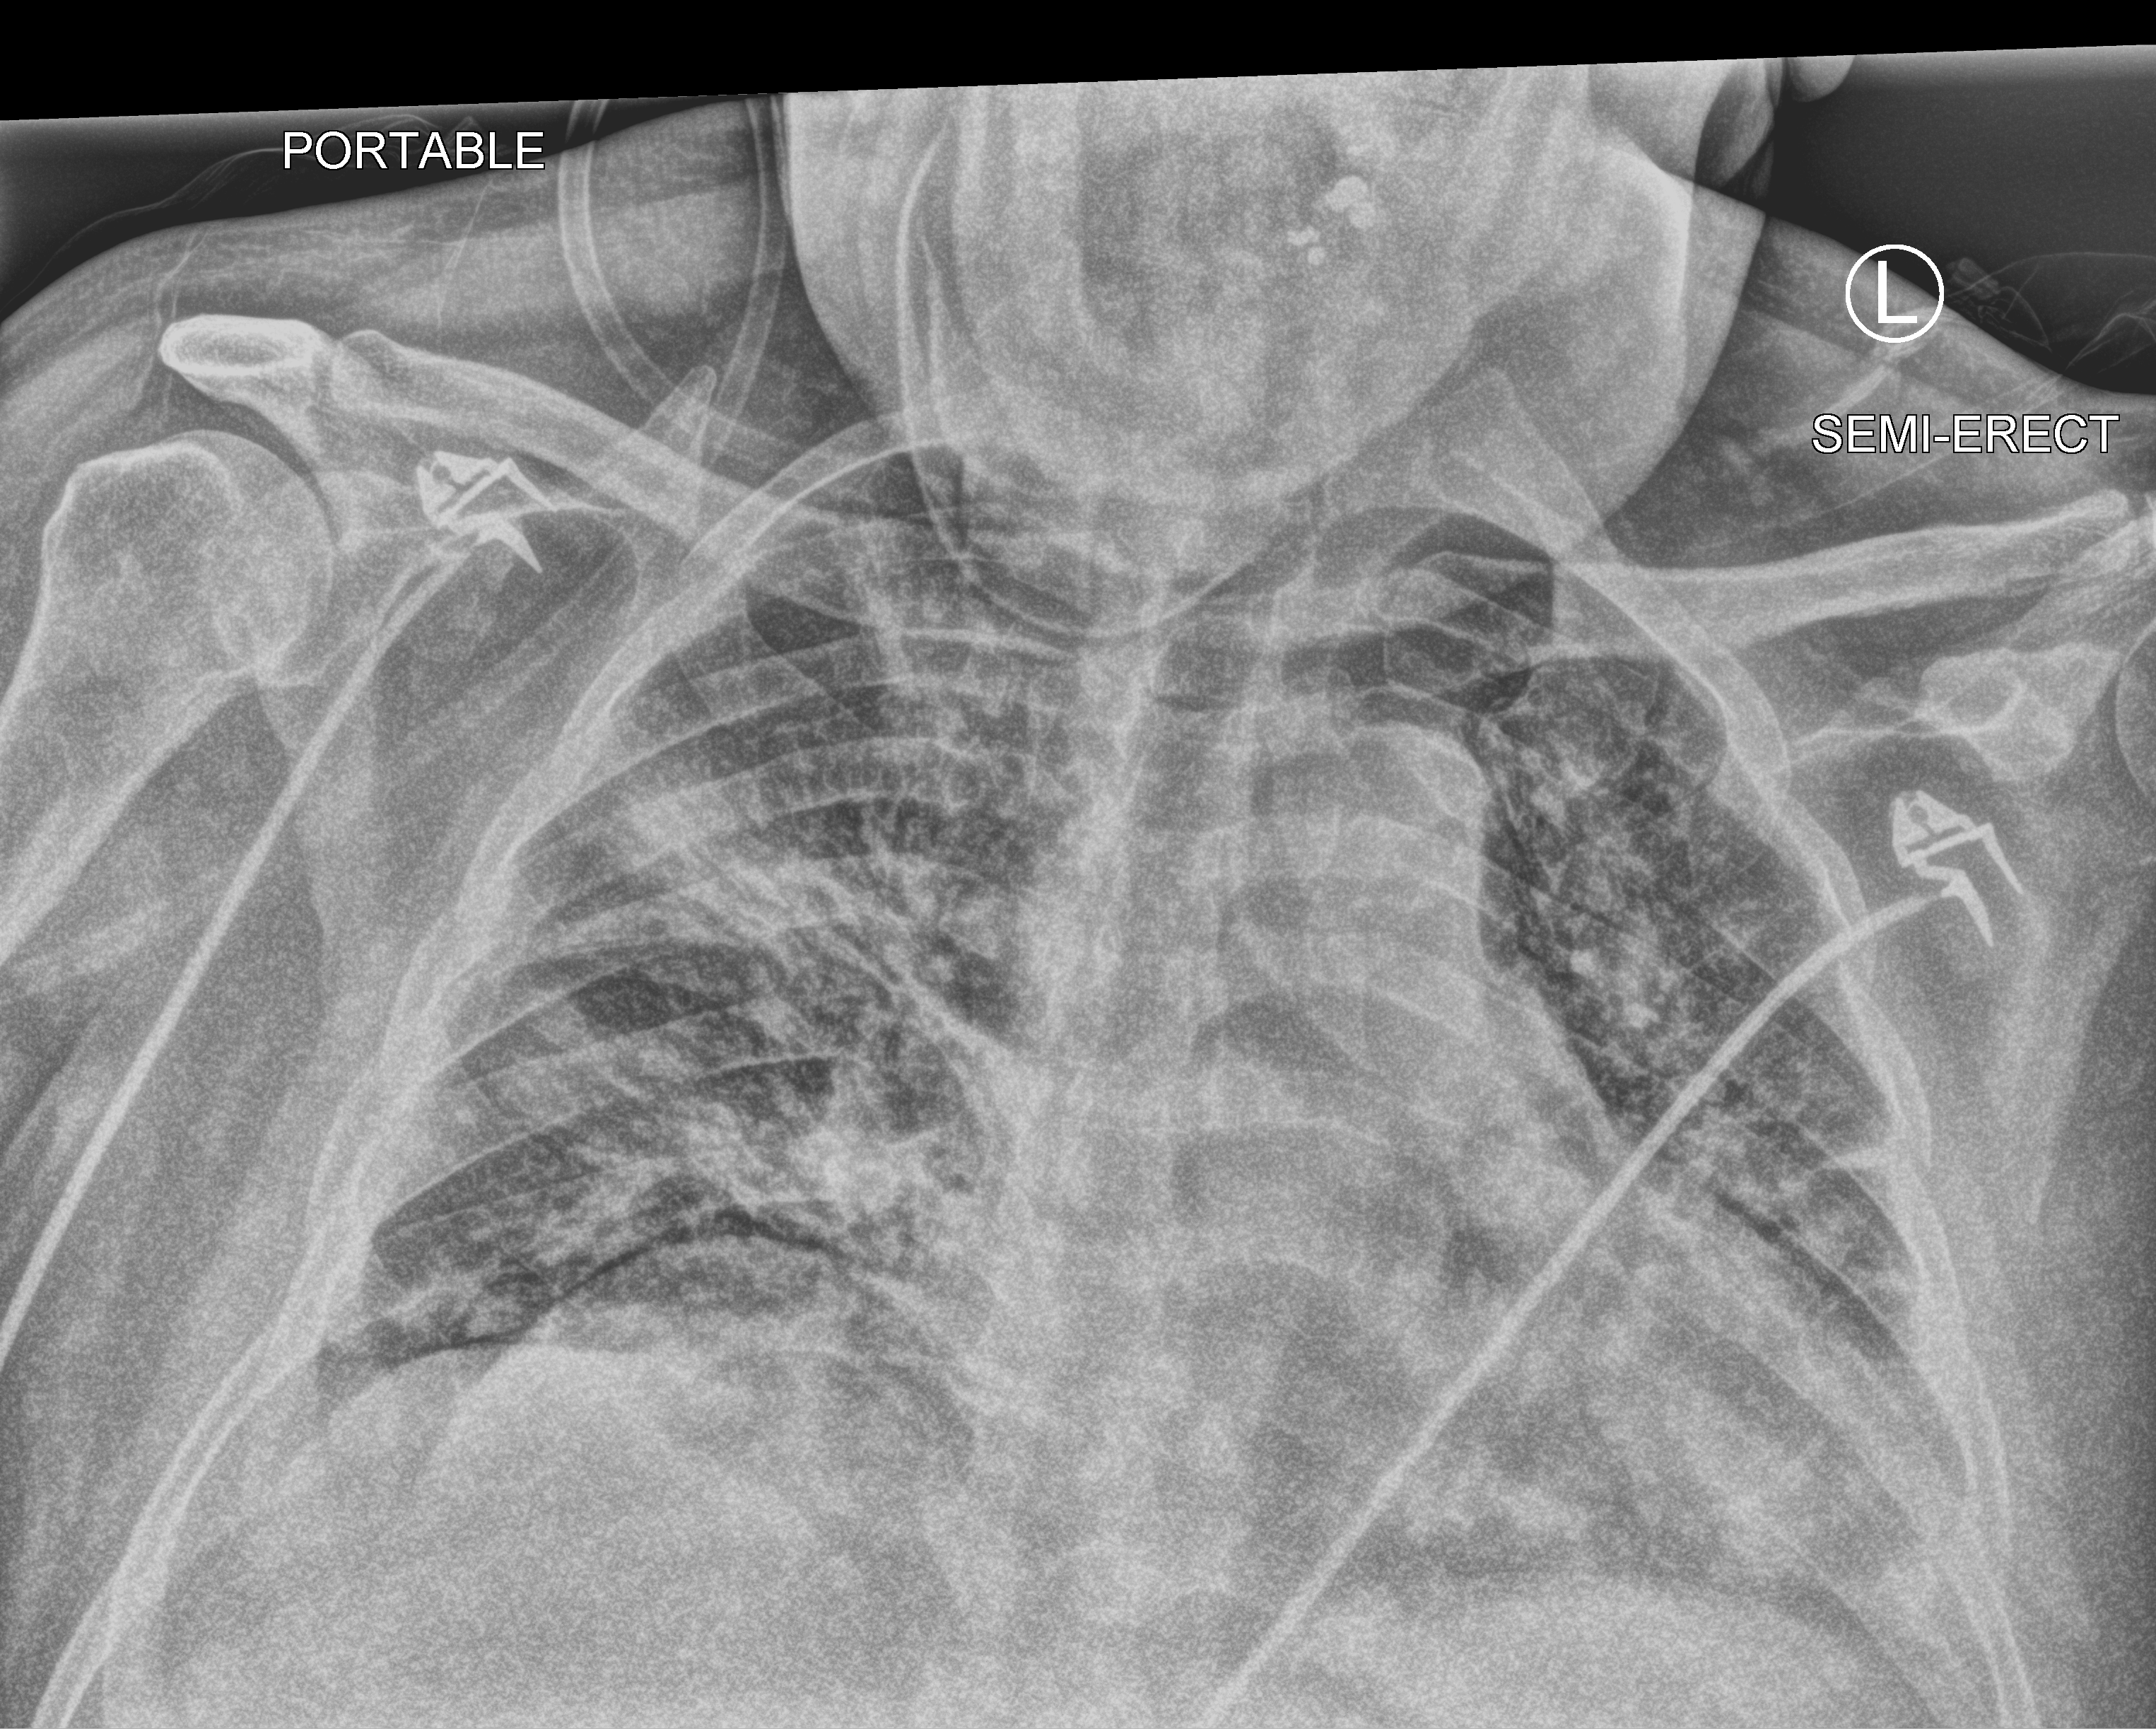
Portable chest radiograph, anteroposterior (AP) projection. Male patient hospitalised with COVID-19, age 60–74 years.
From the hospital-stay record, not from the radiograph (when in the stay this image was taken is not recorded): mechanically ventilated during this hospital stay: yes; length of hospital stay: 28 days; admitted to intensive care during this hospital stay: yes.